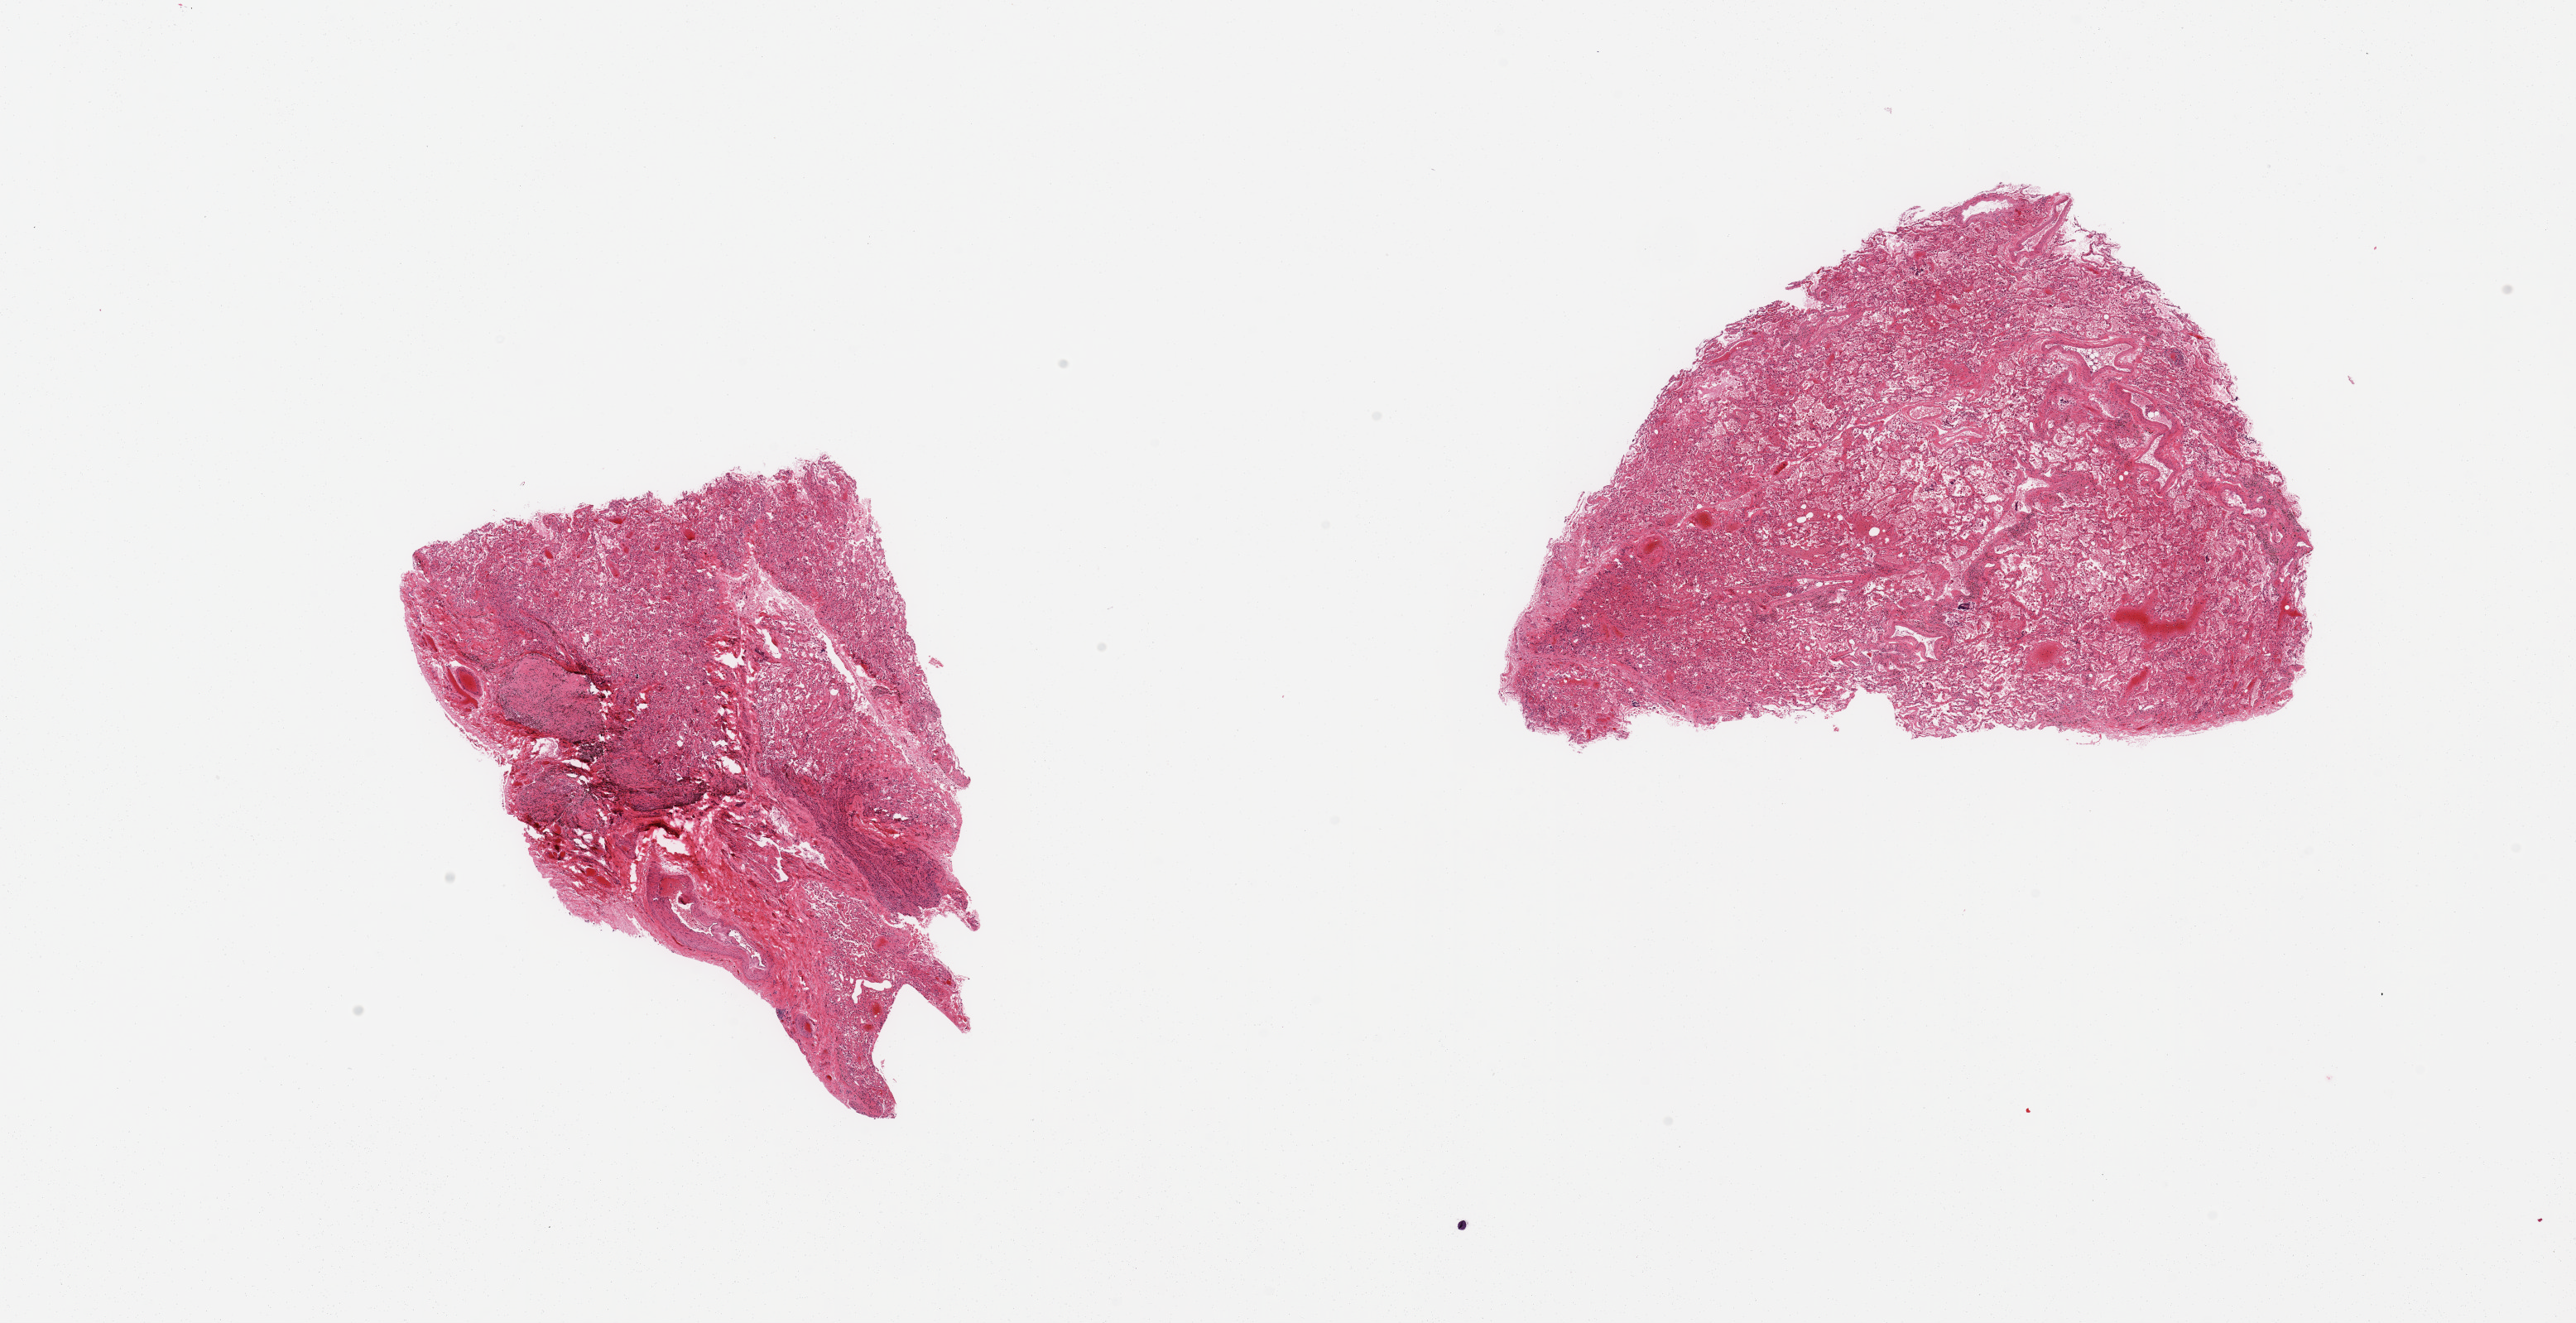
Digitized haematoxylin and eosin-stained section, brightfield, a low-resolution overview of the entire scanned area, about 24.6 x 12.6 mm (from a 20x scan). PAXgene-fixed, paraffin-embedded tissue. Target tissue: lung. Tissue donor sample. Donor: male.
Reviewer comment on this tissue sample: 2 pieces, moderate/marked edema/congestion.